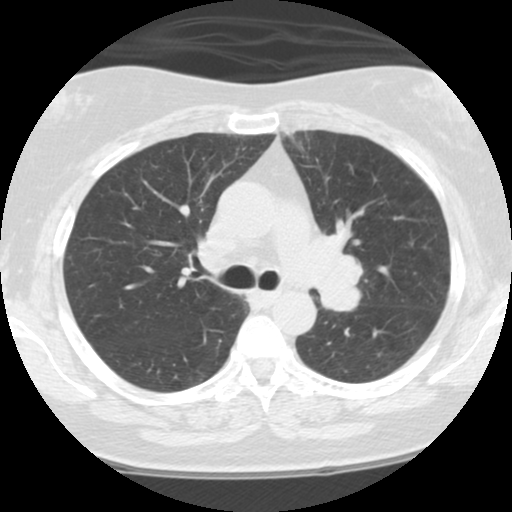
Low-dose screening chest CT, one axial slice. Position 72 of 108 along the scan axis. Reconstruction kernel STANDARD. 120 kVp. Lung window (W 1500 / L -600 HU). 2.5 mm slice thickness. 512 × 512 image matrix, field of view 300 × 300 mm.
Annotated regions visible in this slice (outlined manually by an expert reader):
- lesion 1 (tumor, hilum of left lung): bounding box (x1, y1, x2, y2) in pixels: (321, 255, 362, 311)